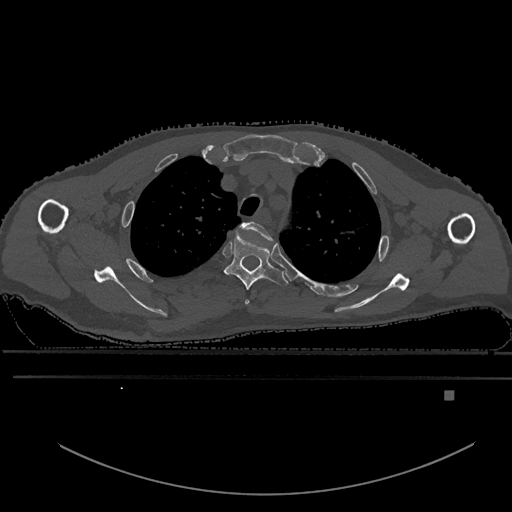
CT including the spine, one axial slice. Slice 458 of 969 in the series (ordered by position). Bone window (W 1800 / L 400 HU). 0.5 mm slice thickness. 512 × 512 image matrix, field of view 456 × 456 mm. Male patient, age 82 years. From the clinical record (not read from this slice): primary cancer: prostate.
Annotated regions visible in this slice (semi-automatic segmentation, software-assisted and operator-edited):
- T2 vertebra: bounding box [x1, y1, x2, y2] px = [240, 222, 276, 305]
- T3 vertebra: [225, 234, 289, 290]